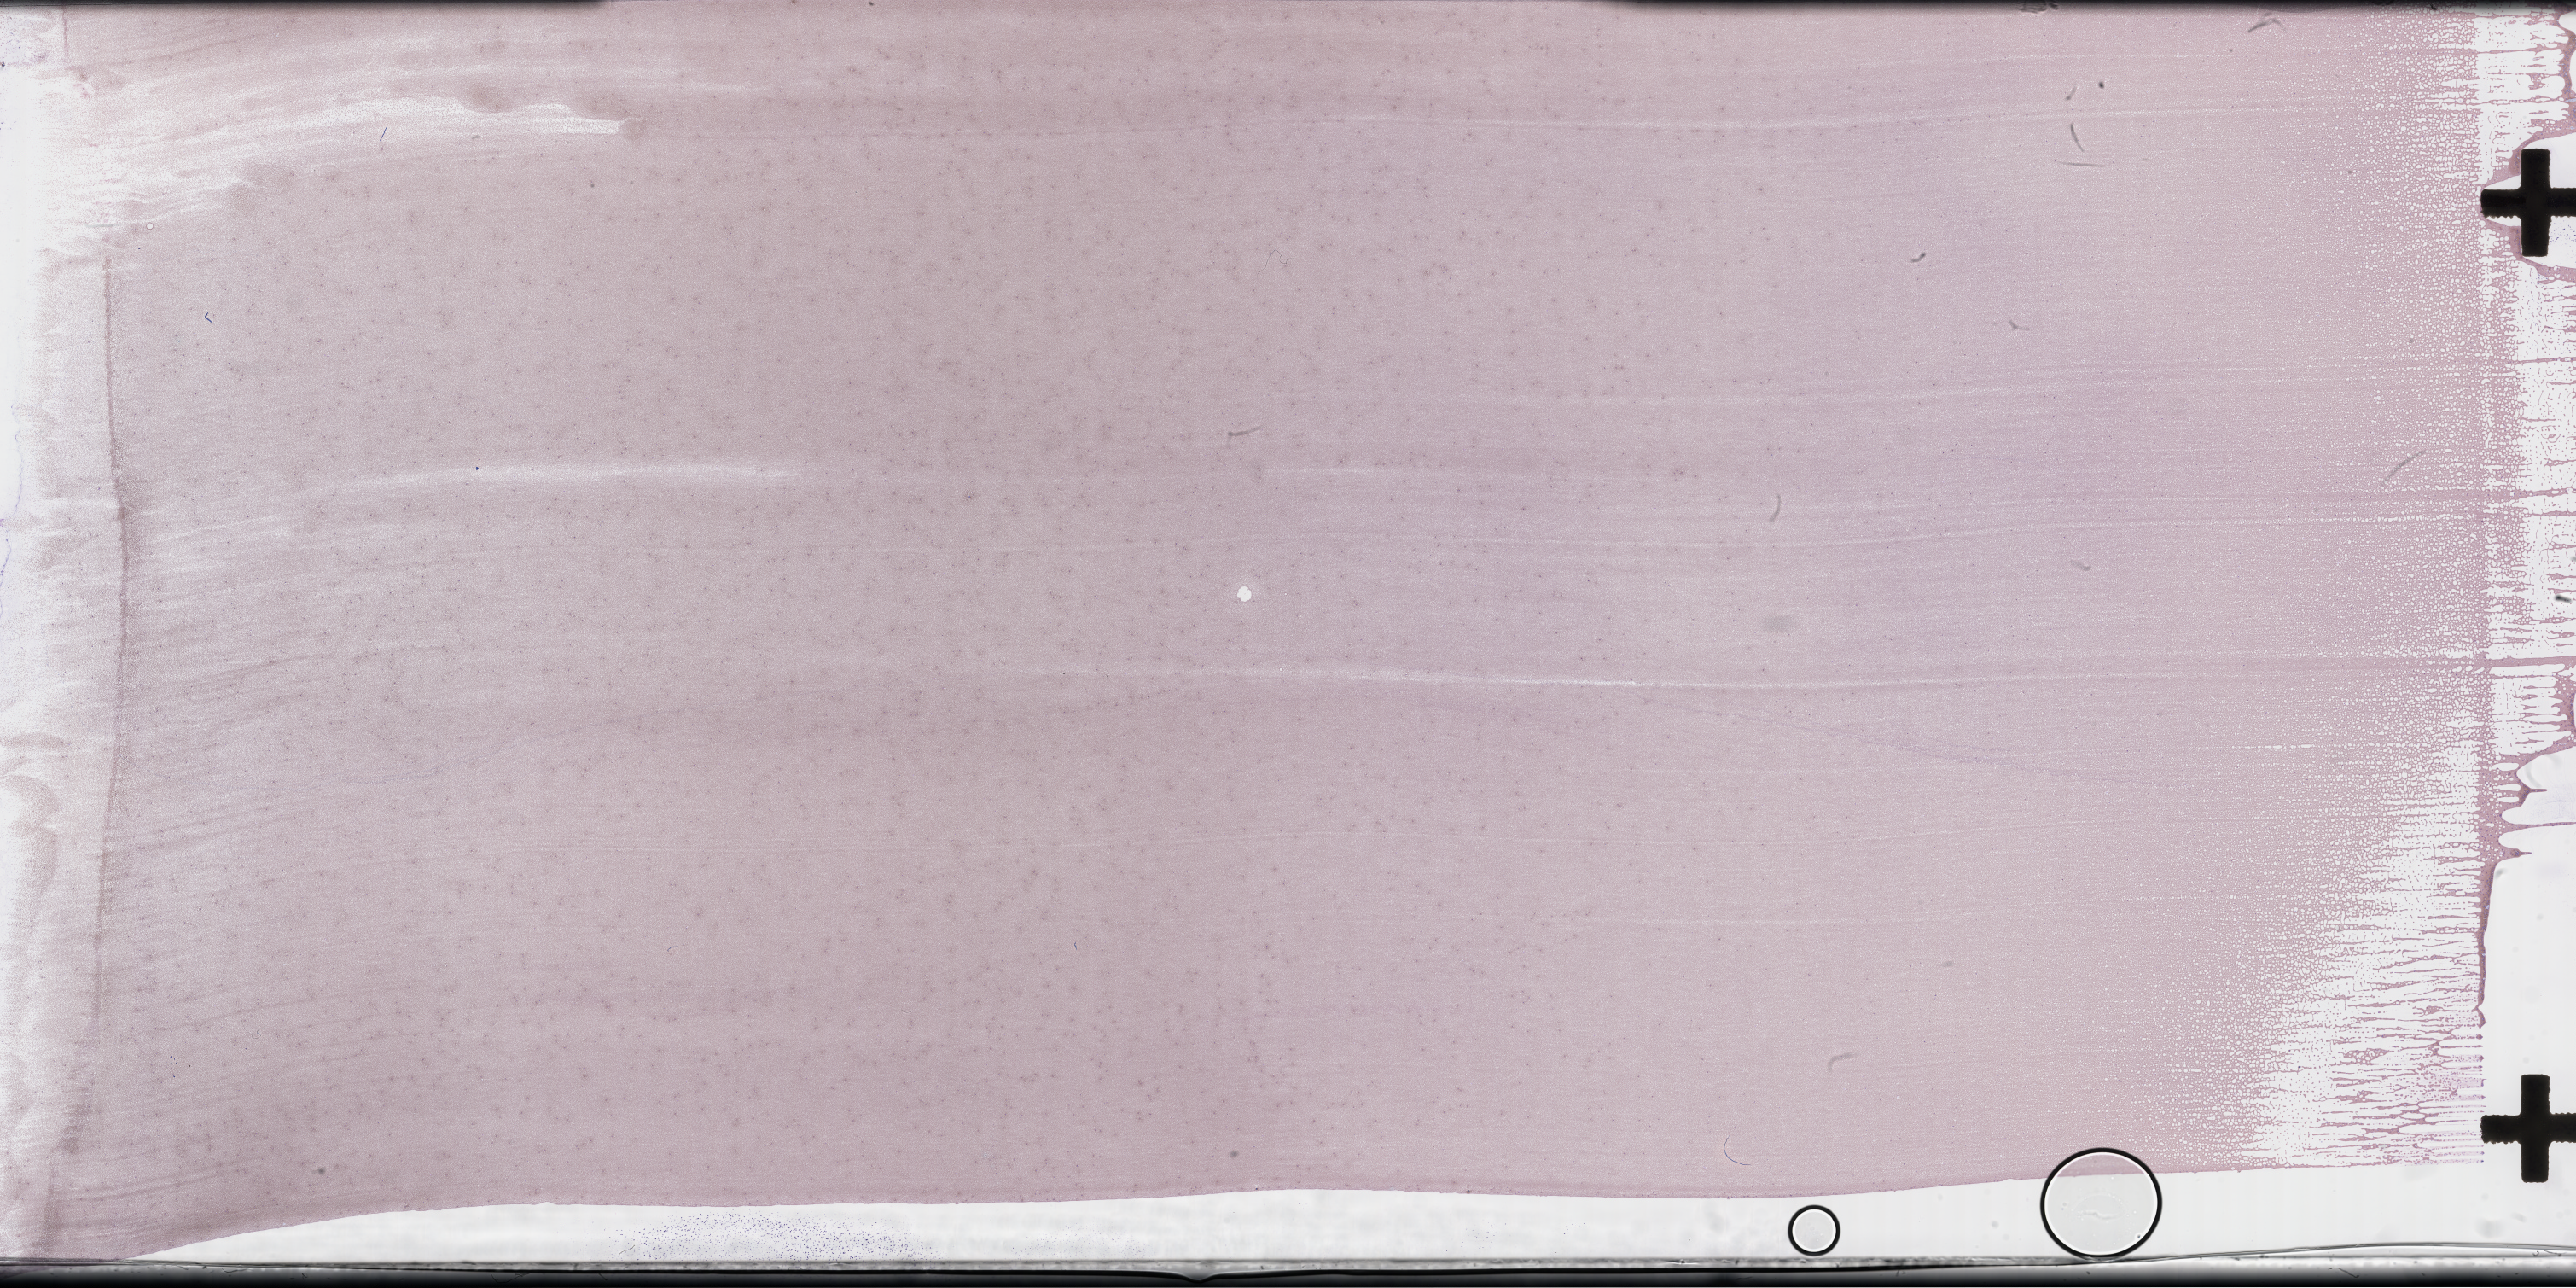
Whole-slide image of a whole blood smear, Wright–Giemsa stain — a low-resolution overview of the entire scanned area, about 48.8 x 24.4 mm. Smear from an EDTA sample. Patient sex: male.
Patient diagnosis: Plasma Cell Myeloma.